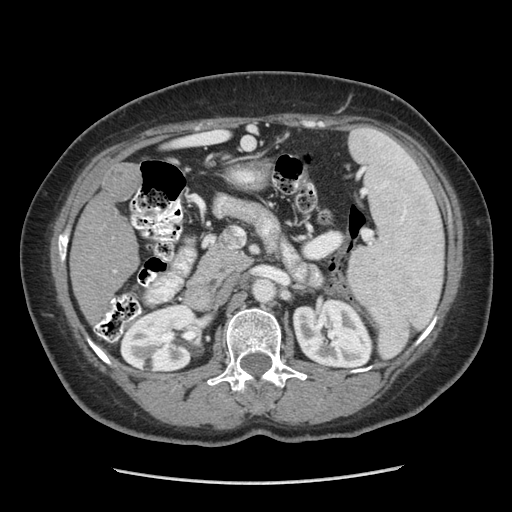
Contrast-enhanced abdominal CT (liver protocol), one axial slice. Slice 133 of 185 in the series (ordered by position). Reconstruction kernel STANDARD. 140 kVp. Soft-tissue window (W 400 / L 40 HU). 2.5 mm slice thickness. 512 × 512 image matrix. From the clinical record (not read from this slice): diagnosis: hepatocellular carcinoma (patient treated with transarterial chemoembolisation; whether this scan precedes or follows treatment is not stated here); TNM stage (as recorded): Stage-I; Child-Pugh class: A; tumour differentiation: poorly differentiated; tumour nodularity: uninodular.
Annotated regions visible in this slice (semi-automatic segmentation, software-assisted and operator-edited):
- liver parenchyma outside the tumour (the mass and vessels are separate outlines, so this box may not span the whole liver): bounding box (x1, y1, x2, y2) in pixels: (70, 162, 140, 320)
- mass: (101, 164, 139, 206)
- liver vessels: (114, 270, 116, 272)